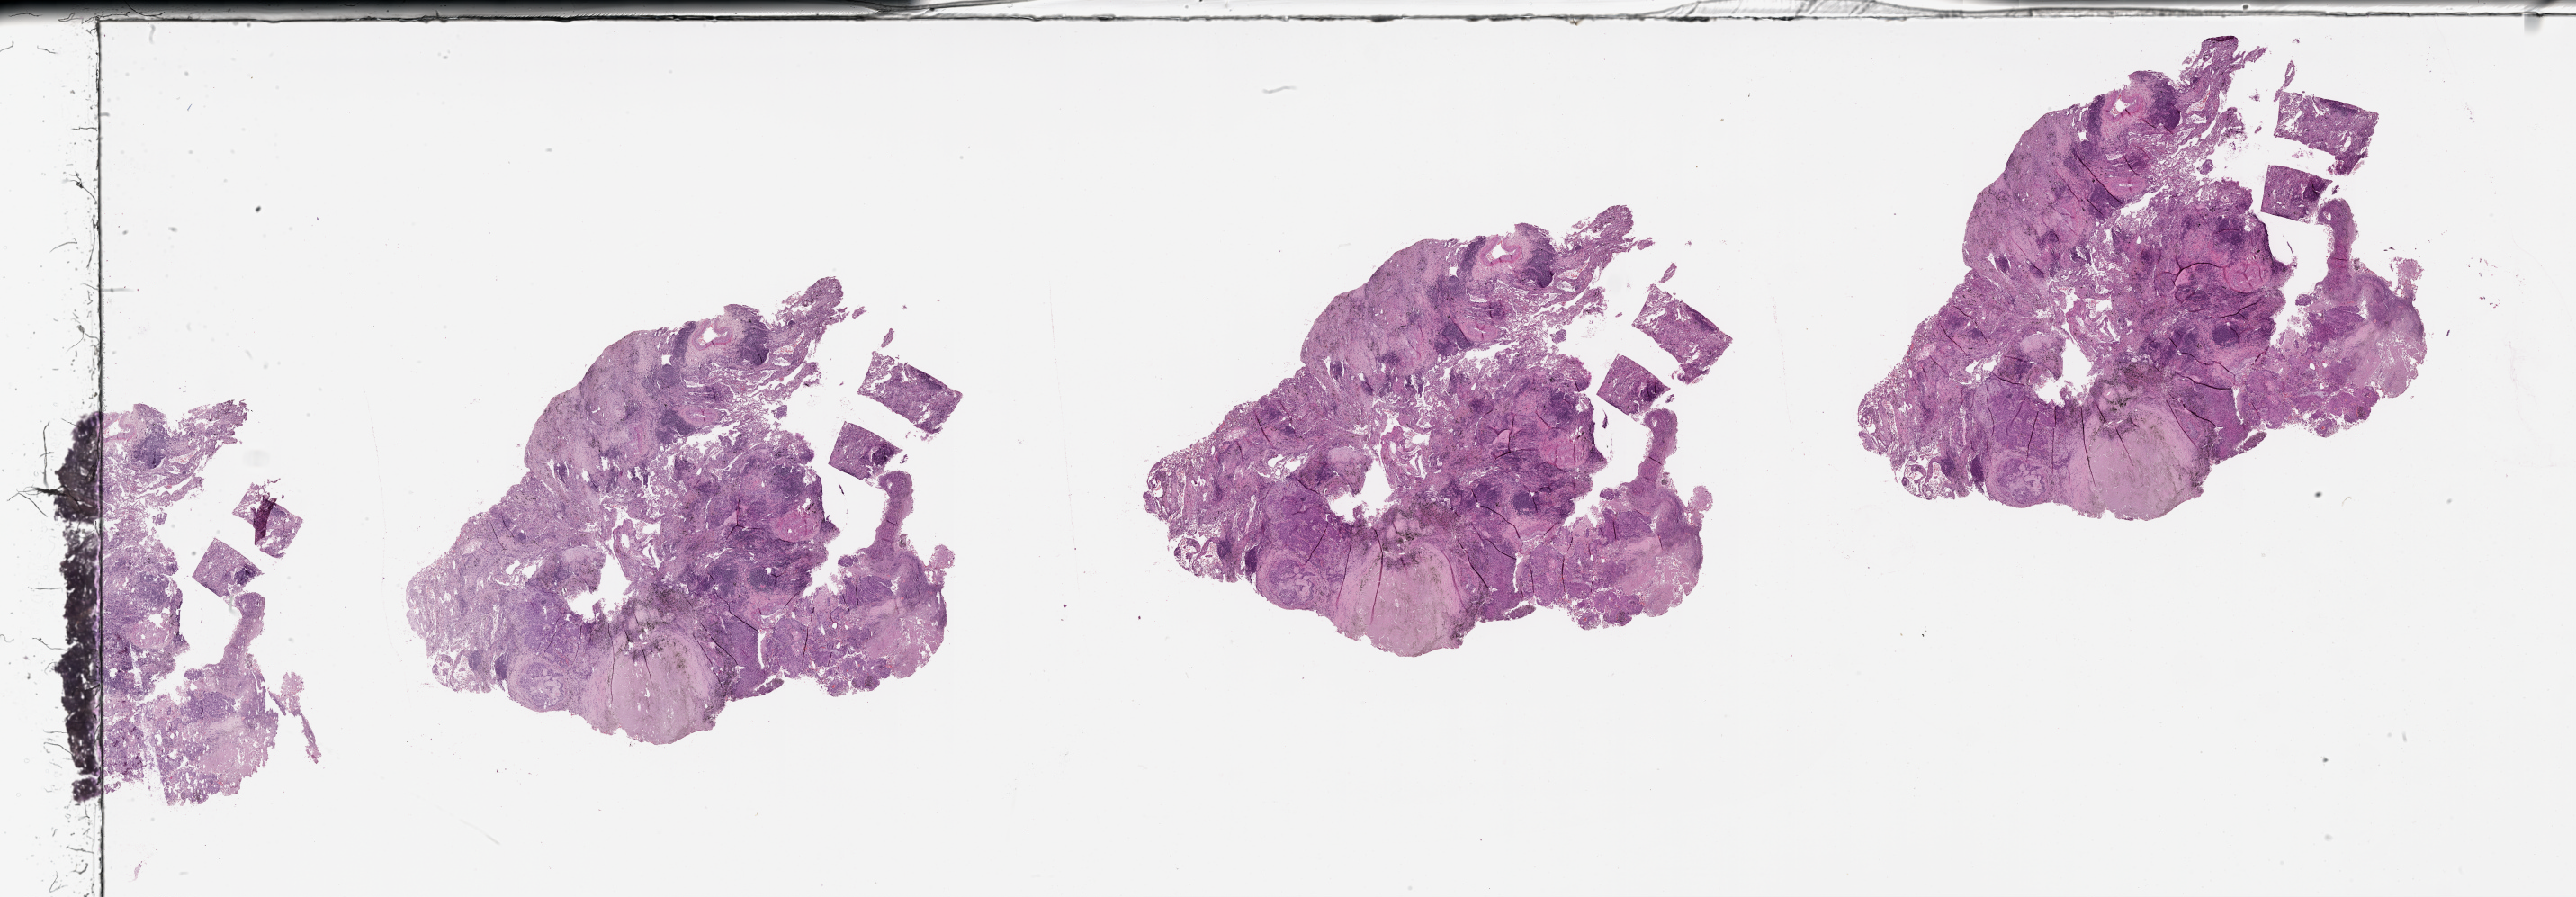
Whole-slide histology image, Hematoxylin and eosin (H&E) stained, whole scanned area (about 46.1 x 16.1 mm) shown as a low-resolution overview. Lung, tumour tissue. 68-year-old male patient.
Patient diagnosis (cohort enrolment): squamous cell carcinoma (lung).